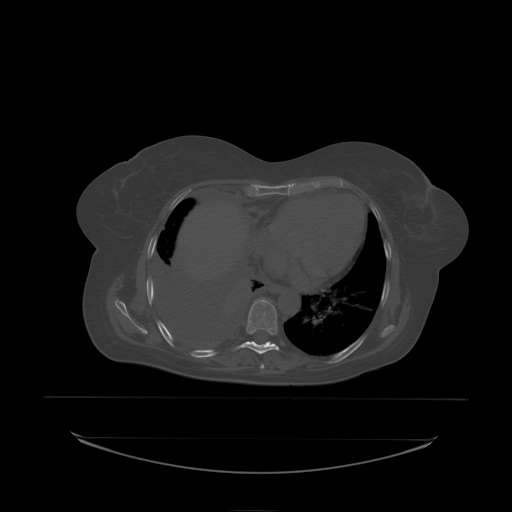
CT including the spine, one axial slice; position 132 of 242 along the scan axis; bone window (W 1800 / L 400 HU); 2.5 mm slice thickness; 512 × 512 image matrix, field of view 500 × 500 mm. Patient: female, 53 years. Case-level facts recorded for this patient, not image findings: primary cancer: lung.
Annotated regions visible in this slice (semi-automatic segmentation, software-assisted and operator-edited):
- T8 vertebra: bounding box <246,299,278,335> (left, top, right, bottom; pixels)